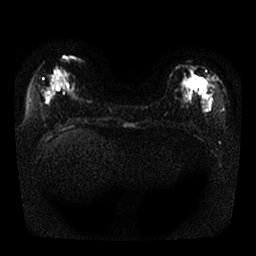
Breast MRI, one axial slice. Position 11 of 25 along the scan axis. Diffusion-weighted series; image 2 of 4 stored at this slice position (different b-values; order by instance number). 1.5 T. 4 mm slice thickness. 256 × 256 image matrix, field of view 330 × 330 mm. Female patient.
Annotated regions visible in this slice (outlined manually by an expert reader):
- tumour on diffusion-weighted imaging: bounding box (x1, y1, x2, y2) in pixels: (183, 76, 202, 91)